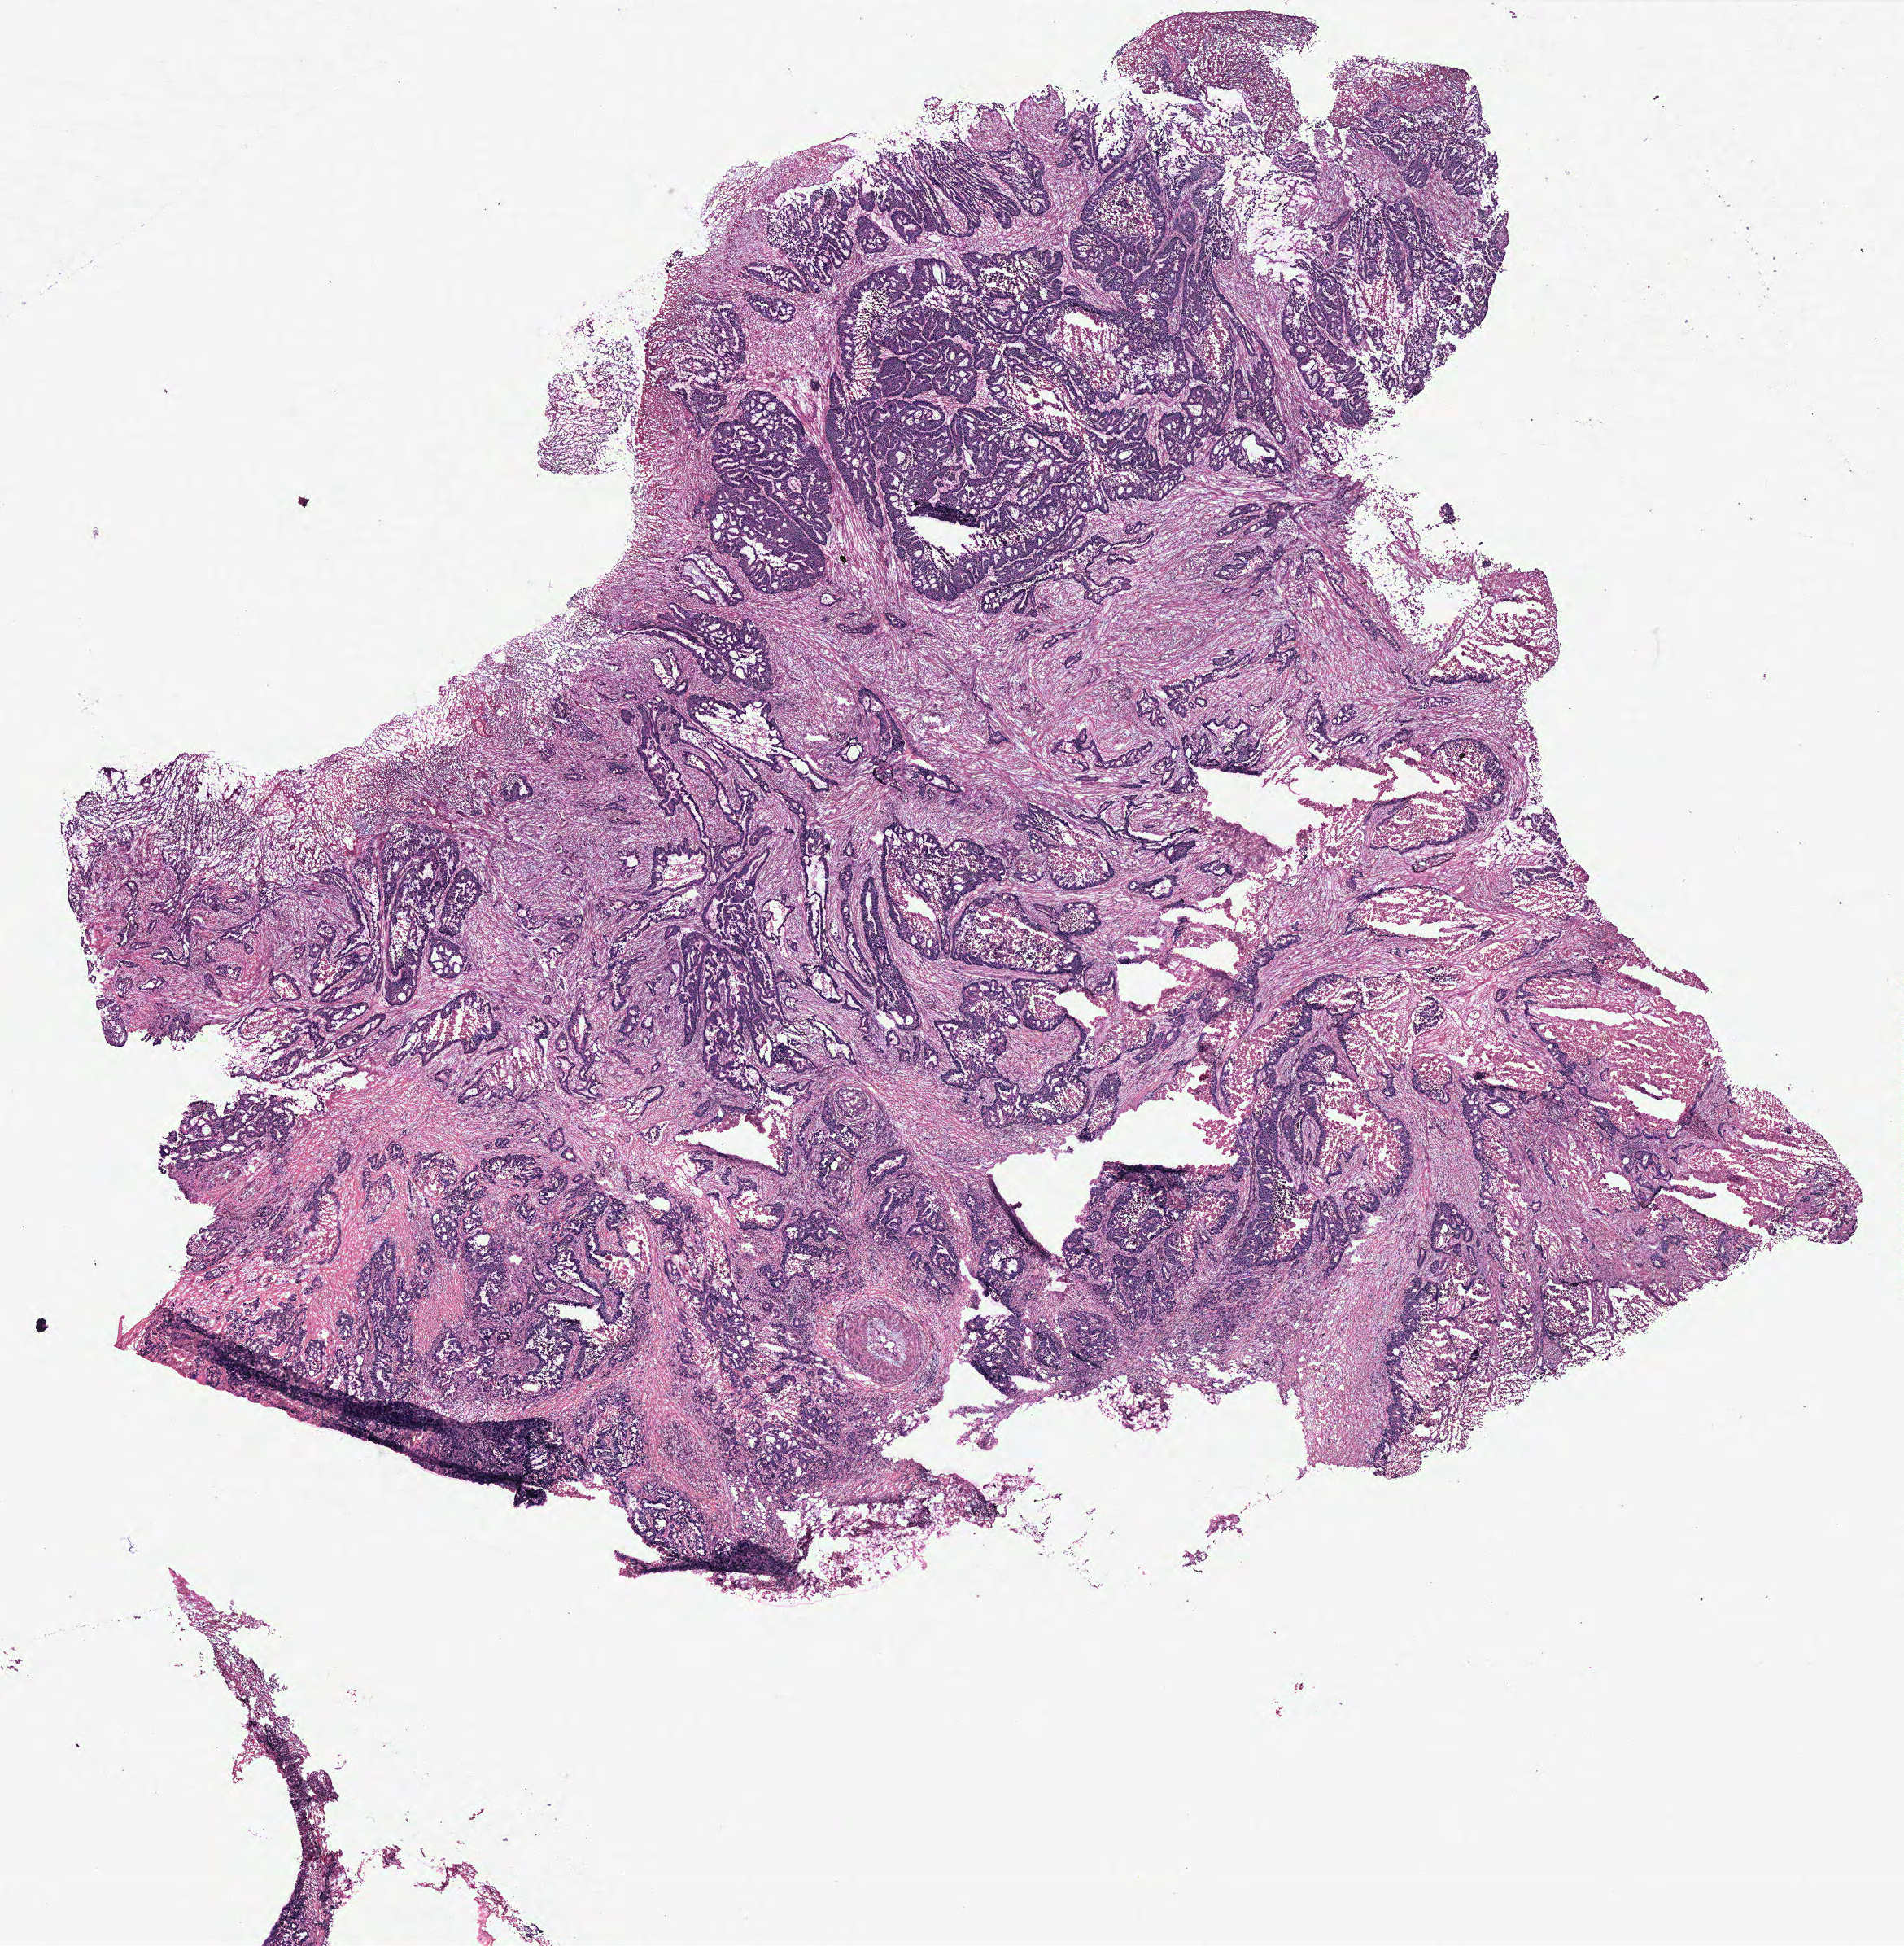
H&E-stained whole-slide image, whole scanned area (about 18.7 x 19.1 mm) shown as a low-resolution overview, tumour tissue sample, colon. Patient: male, age 73 years.
Histologic diagnosis: Adenocarcinoma, NOS.